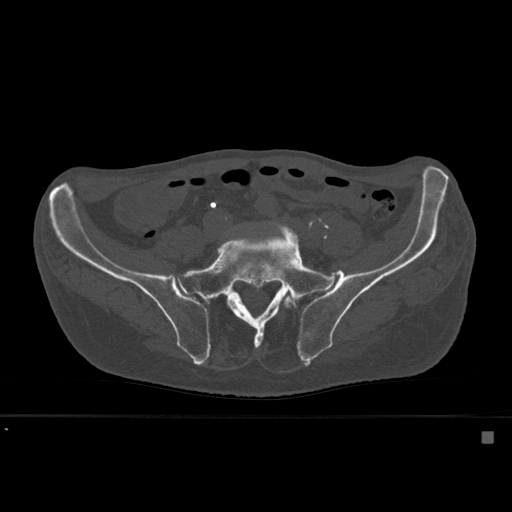
CT including the spine, one axial slice; slice 161 of 527 in the series (ordered by position); bone window (W 1800 / L 400 HU); 1.5 mm slice thickness; 512 × 512 image matrix, field of view 373 × 373 mm. Male patient, age 78 years. From the clinical record (not read from this slice): primary cancer: prostate.
Structures marked on this image (semi-automatic segmentation, software-assisted and operator-edited):
- L5 vertebra: bounding box [x1, y1, x2, y2] px = [283, 291, 296, 308]